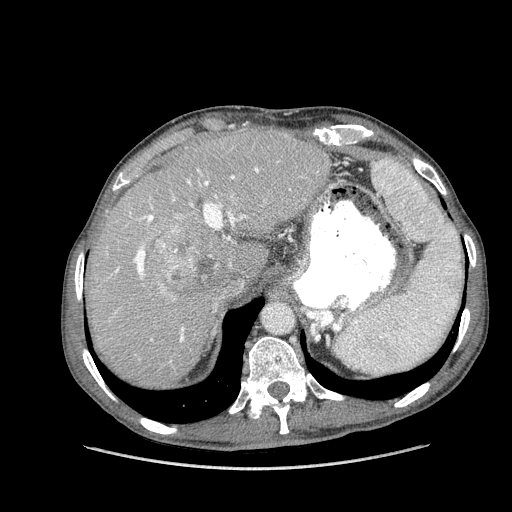
Contrast-enhanced abdominal CT (liver protocol), one axial slice. Position 111 of 162 along the scan axis. Soft-tissue window (W 400 / L 40 HU). 512 × 512 image matrix, field of view 400 × 400 mm. Case-level facts recorded for this patient, not image findings: diagnosis: hepatocellular carcinoma (patient treated with transarterial chemoembolisation; whether this scan precedes or follows treatment is not stated here); TNM stage (as recorded): Stage-IIIA; Child-Pugh class: A; tumour nodularity: multinodular; tumour size: 9.9 cm.
Annotated regions visible in this slice (semi-automatically segmented with operator editing):
- liver parenchyma outside the tumour (the mass and vessels are separate outlines, so this box may not span the whole liver): bounding box <86,126,330,386> (left, top, right, bottom; pixels)
- mass: <154,231,245,299>
- liver vessels: <115,167,259,362>